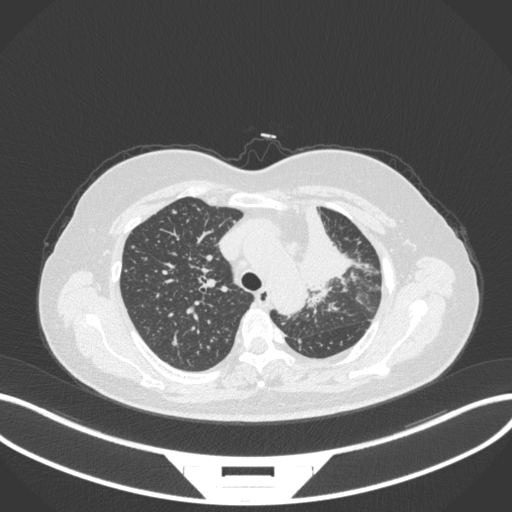
Chest CT, one axial slice. Slice 247 of 348 in the series (ordered by position). 120 kVp. Lung window (W 1500 / L -600 HU). 512 × 512 image matrix, field of view 400 × 400 mm. Patient: female, 49 years. From the clinical record (not read from this slice): clinical TNM (as recorded): T1c N0 M1.
Annotated regions visible in this slice (bounding box drawn by a radiologist):
- lung tumour (recorded histology: adenocarcinoma): box from (x=293, y=200) to (x=359, y=296) px